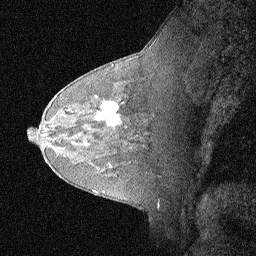
Breast MRI (dynamic contrast-enhanced), one sagittal slice. Slice 42 of 64 in the series (ordered by position). Dynamic contrast-enhanced study with each time point stored as its own series, time point 2 of 3 at this slice position (early post-contrast, ordered by acquisition time). 1.5 T. TE 4.5 ms, TR 11 ms. 2.06 mm slice thickness. 256 × 256 image matrix, field of view 200 × 200 mm. Female patient, age 62 years. From the clinical record (not read from this slice): setting: breast cancer imaged before/during neoadjuvant chemotherapy; receptor status: HR-positive, HER2-negative.
Annotated regions visible in this slice (semi-automatic segmentation, software-assisted and operator-edited):
- analysis volume of interest (the breast-tissue region the enhancement analysis was run in; not a lesion): box from (x=91, y=93) to (x=124, y=129) px
- tumour enhancement mask (voxels above the 90 % enhancement threshold inside the analysis volume of interest): (x=102, y=102)–(x=121, y=125)